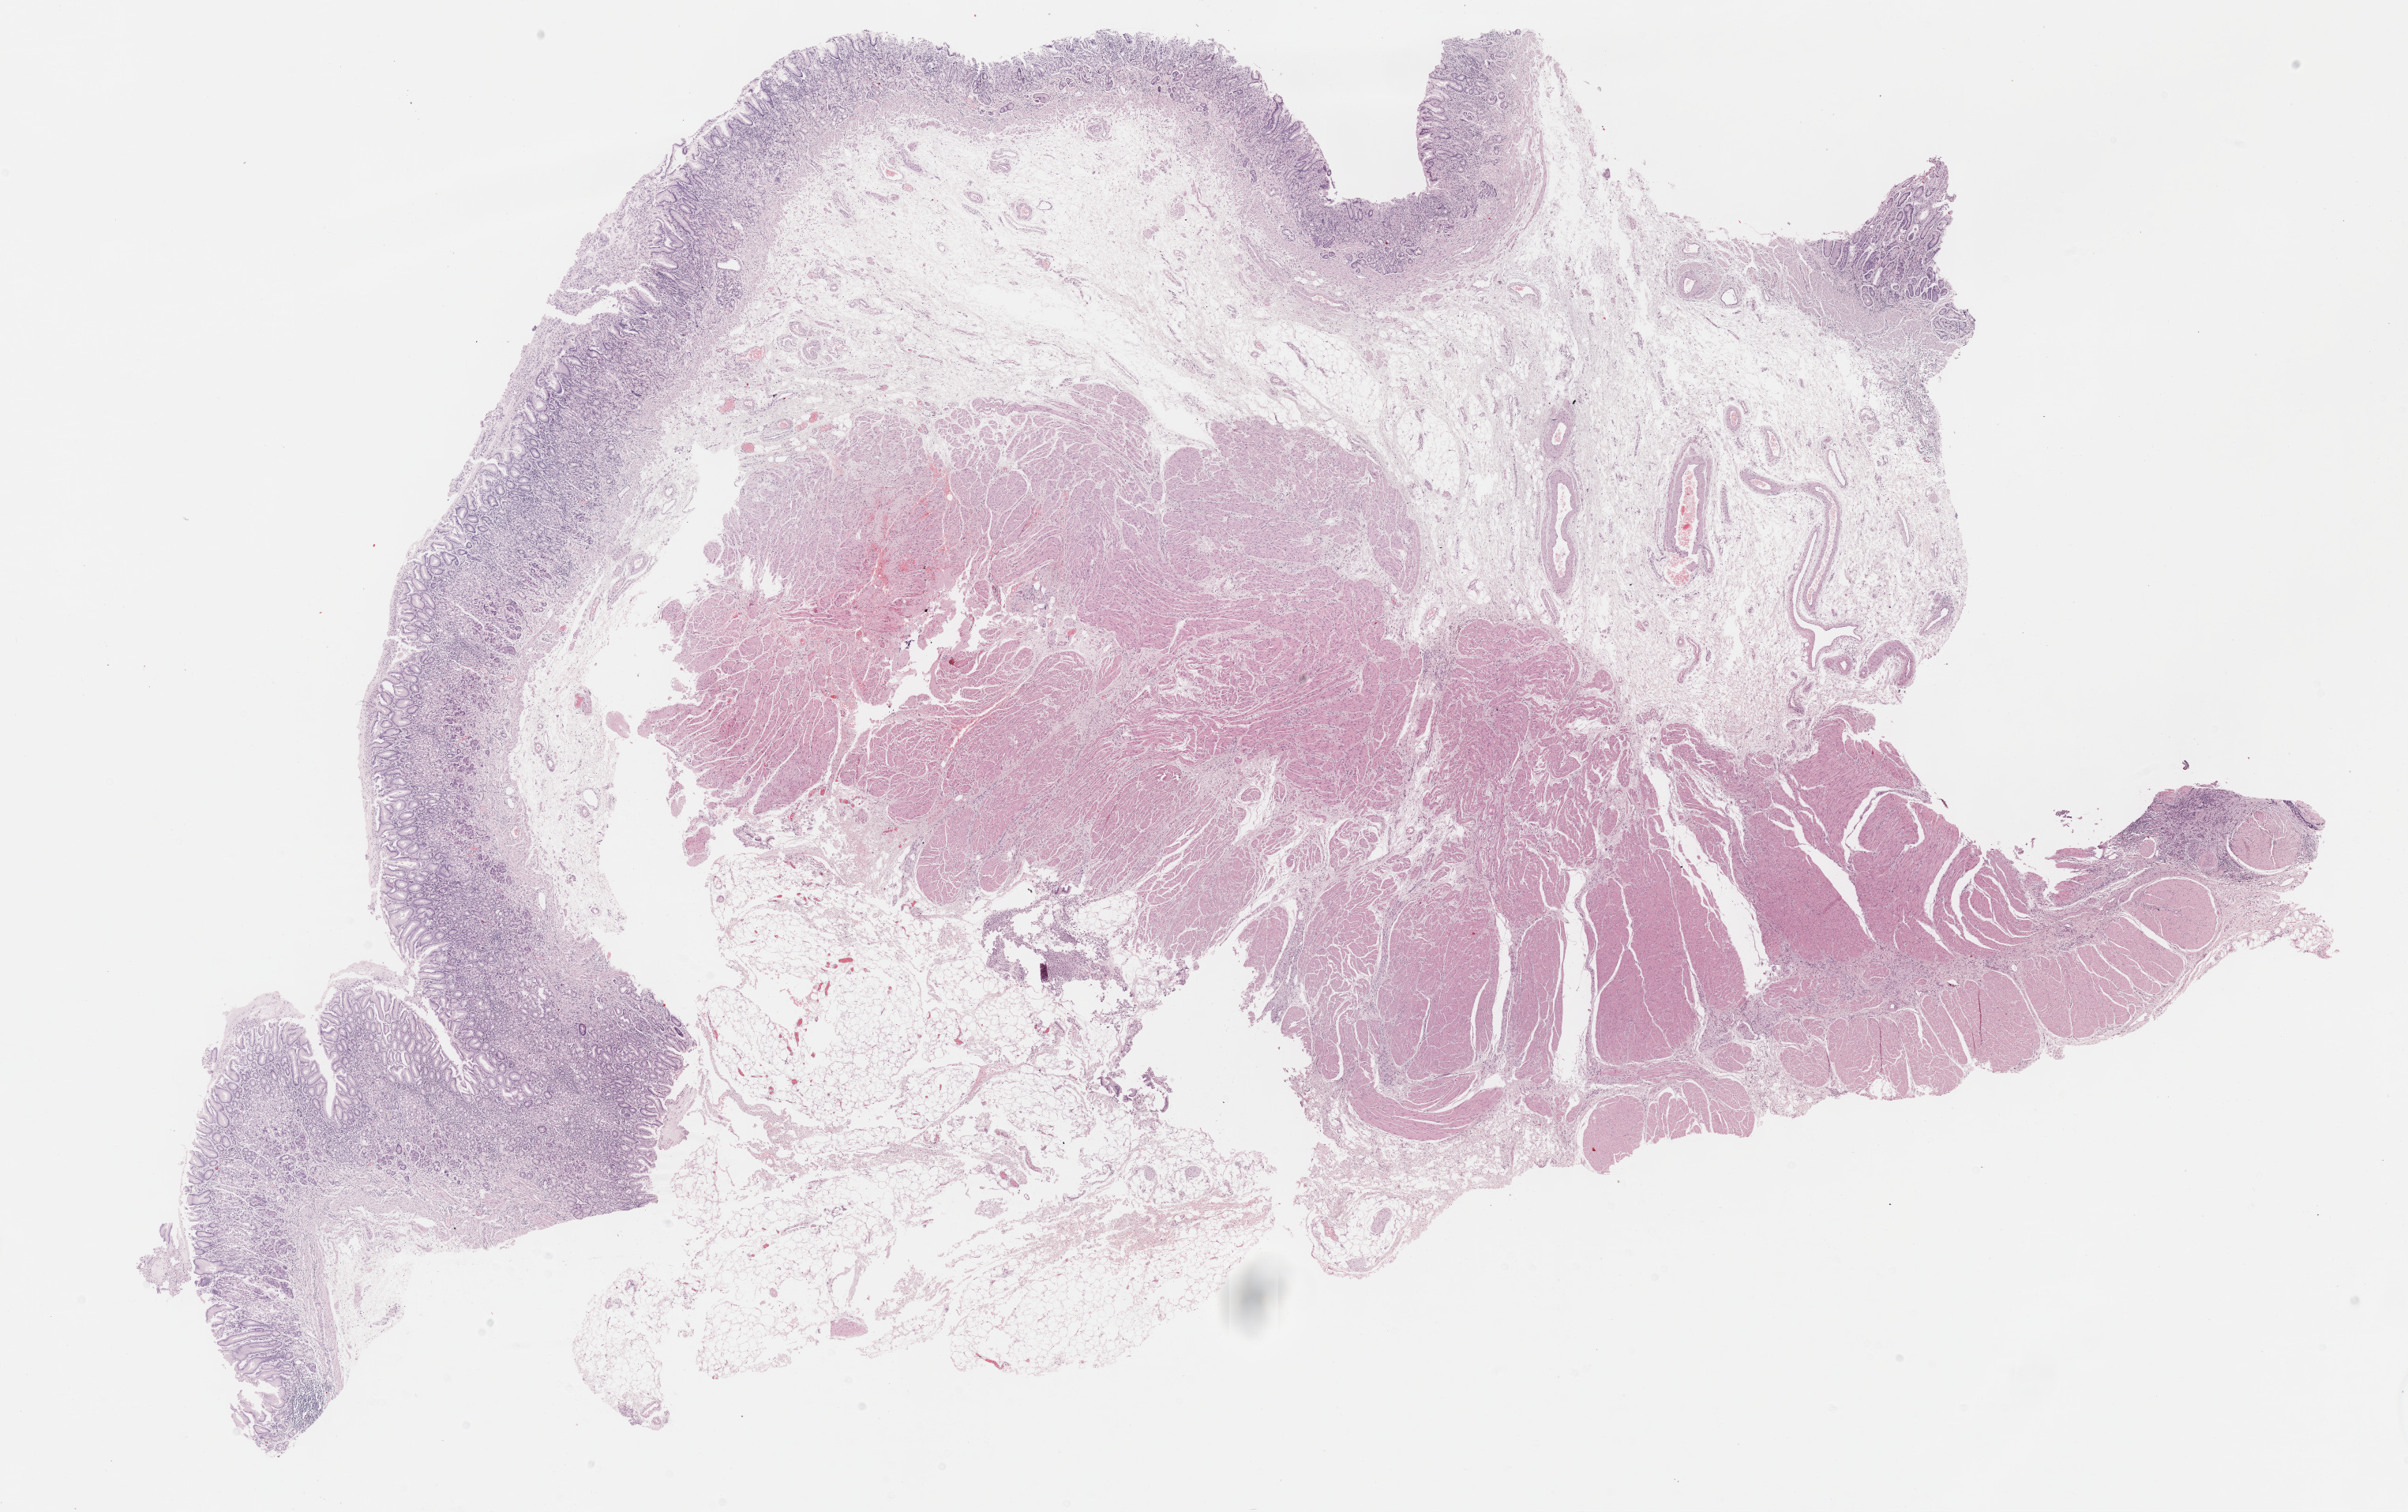
Digitized H&E-stained tissue section (whole slide), whole scanned area (about 24.7 x 15.5 mm) shown as a low-resolution overview, formalin-fixed paraffin-embedded (FFPE) diagnostic section, stomach, primary tumour sample. Female patient; age at initial diagnosis 61 years. Histologic grade: G2 (moderately differentiated).
Diagnosis: Adenocarcinoma, intestinal type (cardia, NOS). AJCC pathologic stage: IIIA.